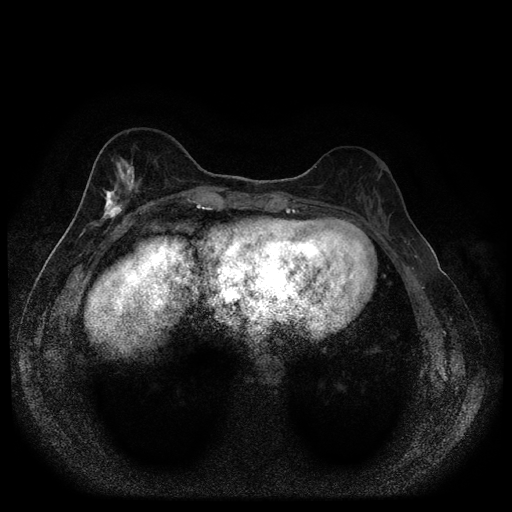
Breast MRI (dynamic contrast-enhanced, multi-phase), one axial slice; position 36 of 116 along the scan axis; dynamic contrast-enhanced series, time point 2 of 5 at this slice position (early post-contrast); 1.5 T; TE 2.7 ms, TR 5.4 ms; 2 mm slice thickness; 512 × 512 image matrix, field of view 330 × 330 mm. Female patient, age 49 years.
Outlined on this slice (semi-automatically segmented with operator editing):
- breast lesion (labelled 'tumour' in the annotation; benign lesions carry a separate 'benign' label): bounding box (x1, y1, x2, y2) in pixels: (90, 157, 143, 230)